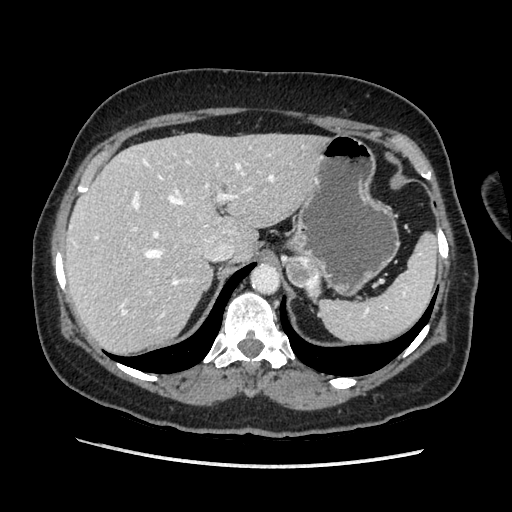
Contrast-enhanced abdominal CT, one axial slice; position 145 of 203 along the scan axis; soft-tissue window (W 400 / L 40 HU); 1.25 mm slice thickness; 512 × 512 image matrix, field of view 360 × 360 mm. Female patient. Case-level facts recorded for this patient, not image findings: diagnosis: adrenocortical carcinoma; tumour side: left adrenal; tumour size at pathology: 6.5 cm; Ki-67 index: 22 %; stage (as recorded): 2.
Outlined on this slice (semi-automatic segmentation, software-assisted and operator-edited):
- mass: box from (x=286, y=257) to (x=321, y=298) px